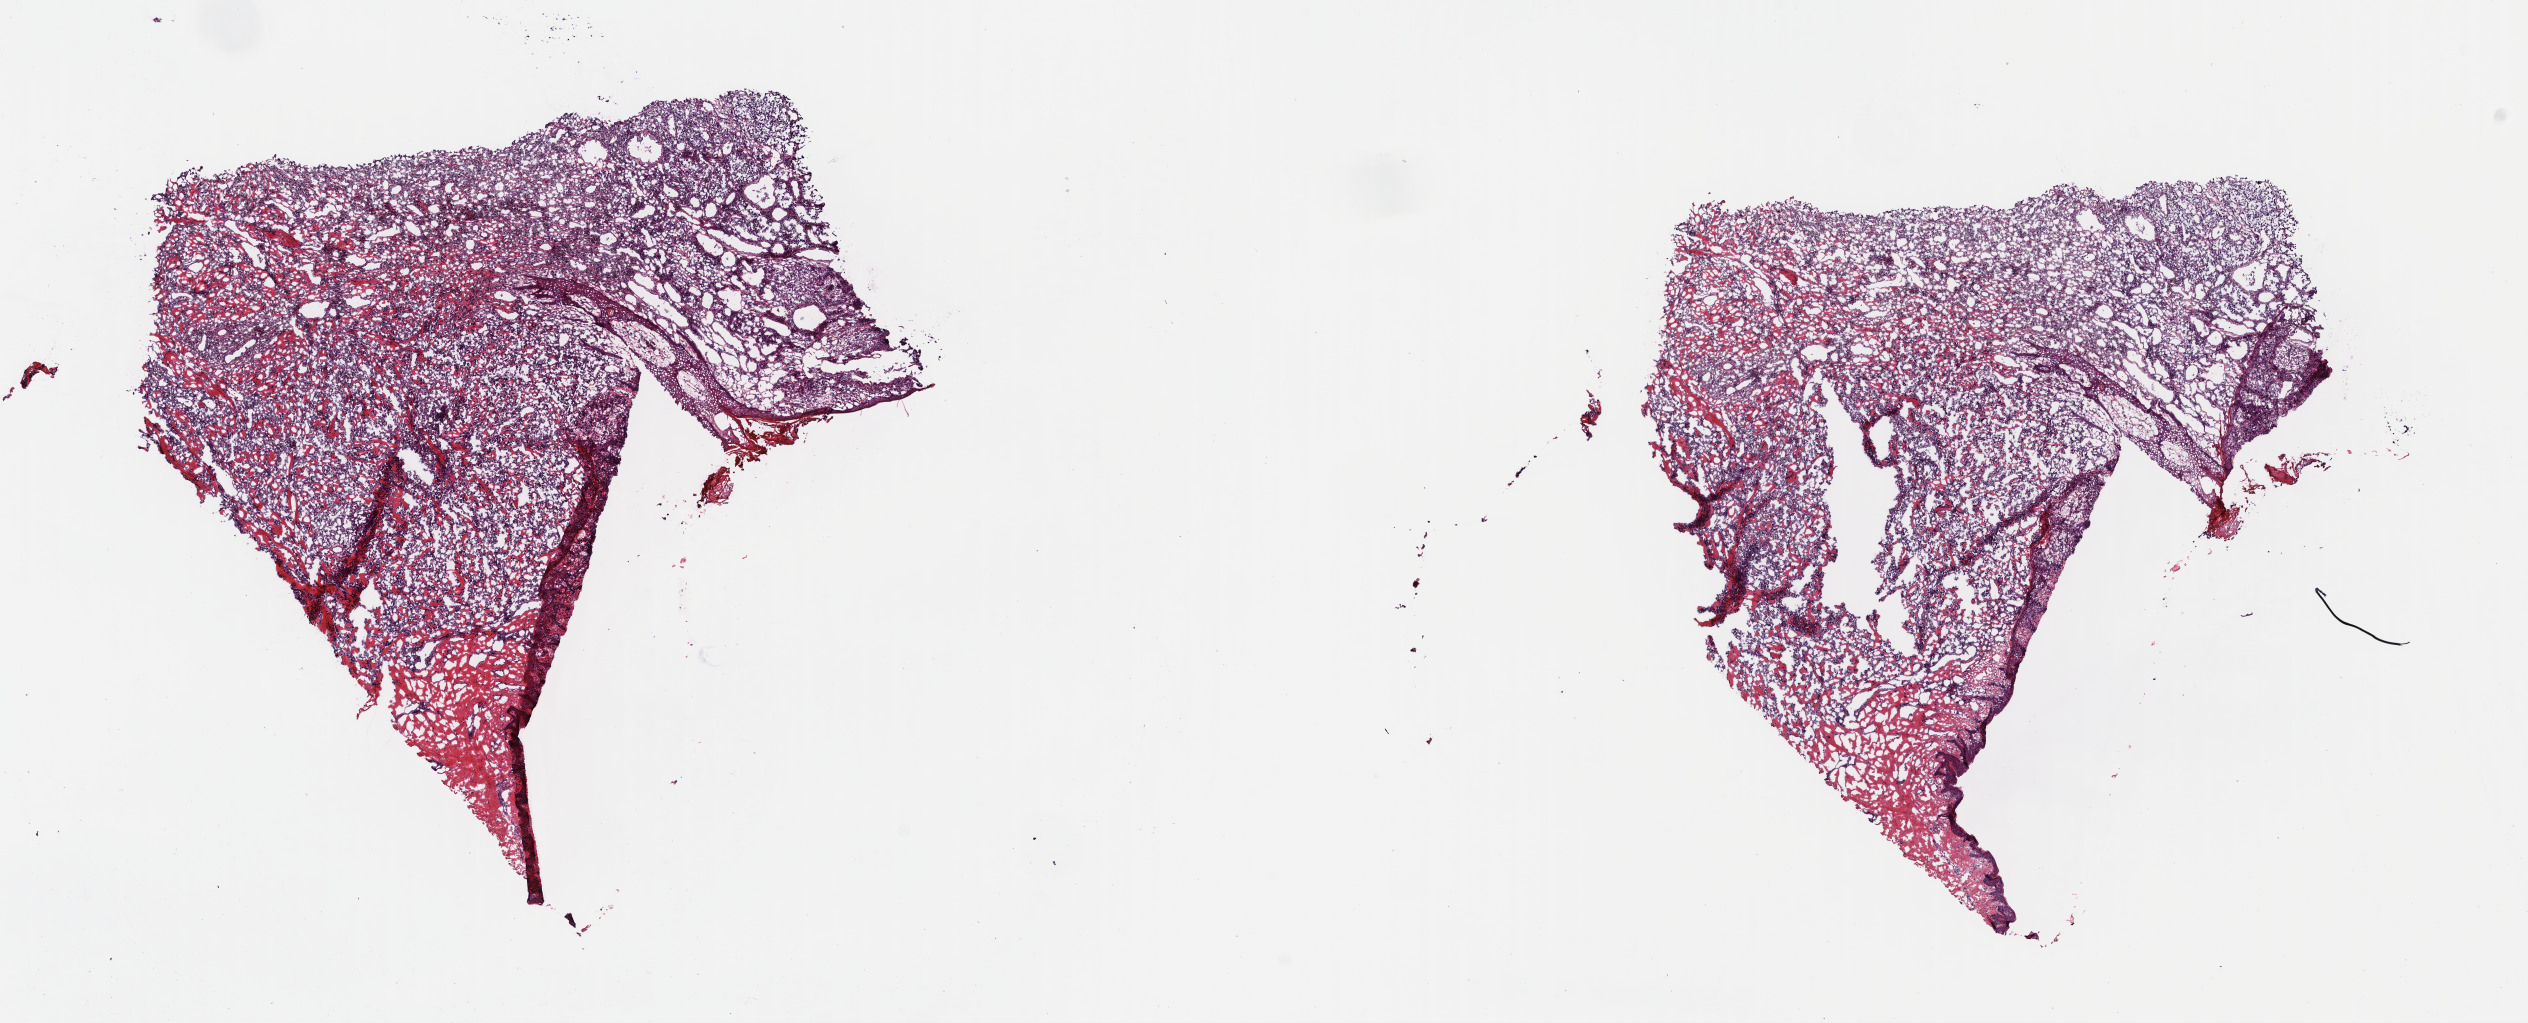
H&E whole-slide image, low-resolution overview of the scanned area, about 19.9 x 8.0 mm. Frozen section from the top of the tissue portion. Primary tumour sample from the skin. Female patient; age at initial diagnosis 41 years. Slide review estimates, as recorded: tumour cells 100%, tumour nuclei 75%, normal cells 0%, stromal cells 0%, necrosis 0%. Infiltration values recorded for this section: lymphocyte infiltration 3%, monocyte infiltration 0%, neutrophil infiltration 0%.
• AJCC pathologic stage: IIIC
• diagnosis: Malignant melanoma, NOS